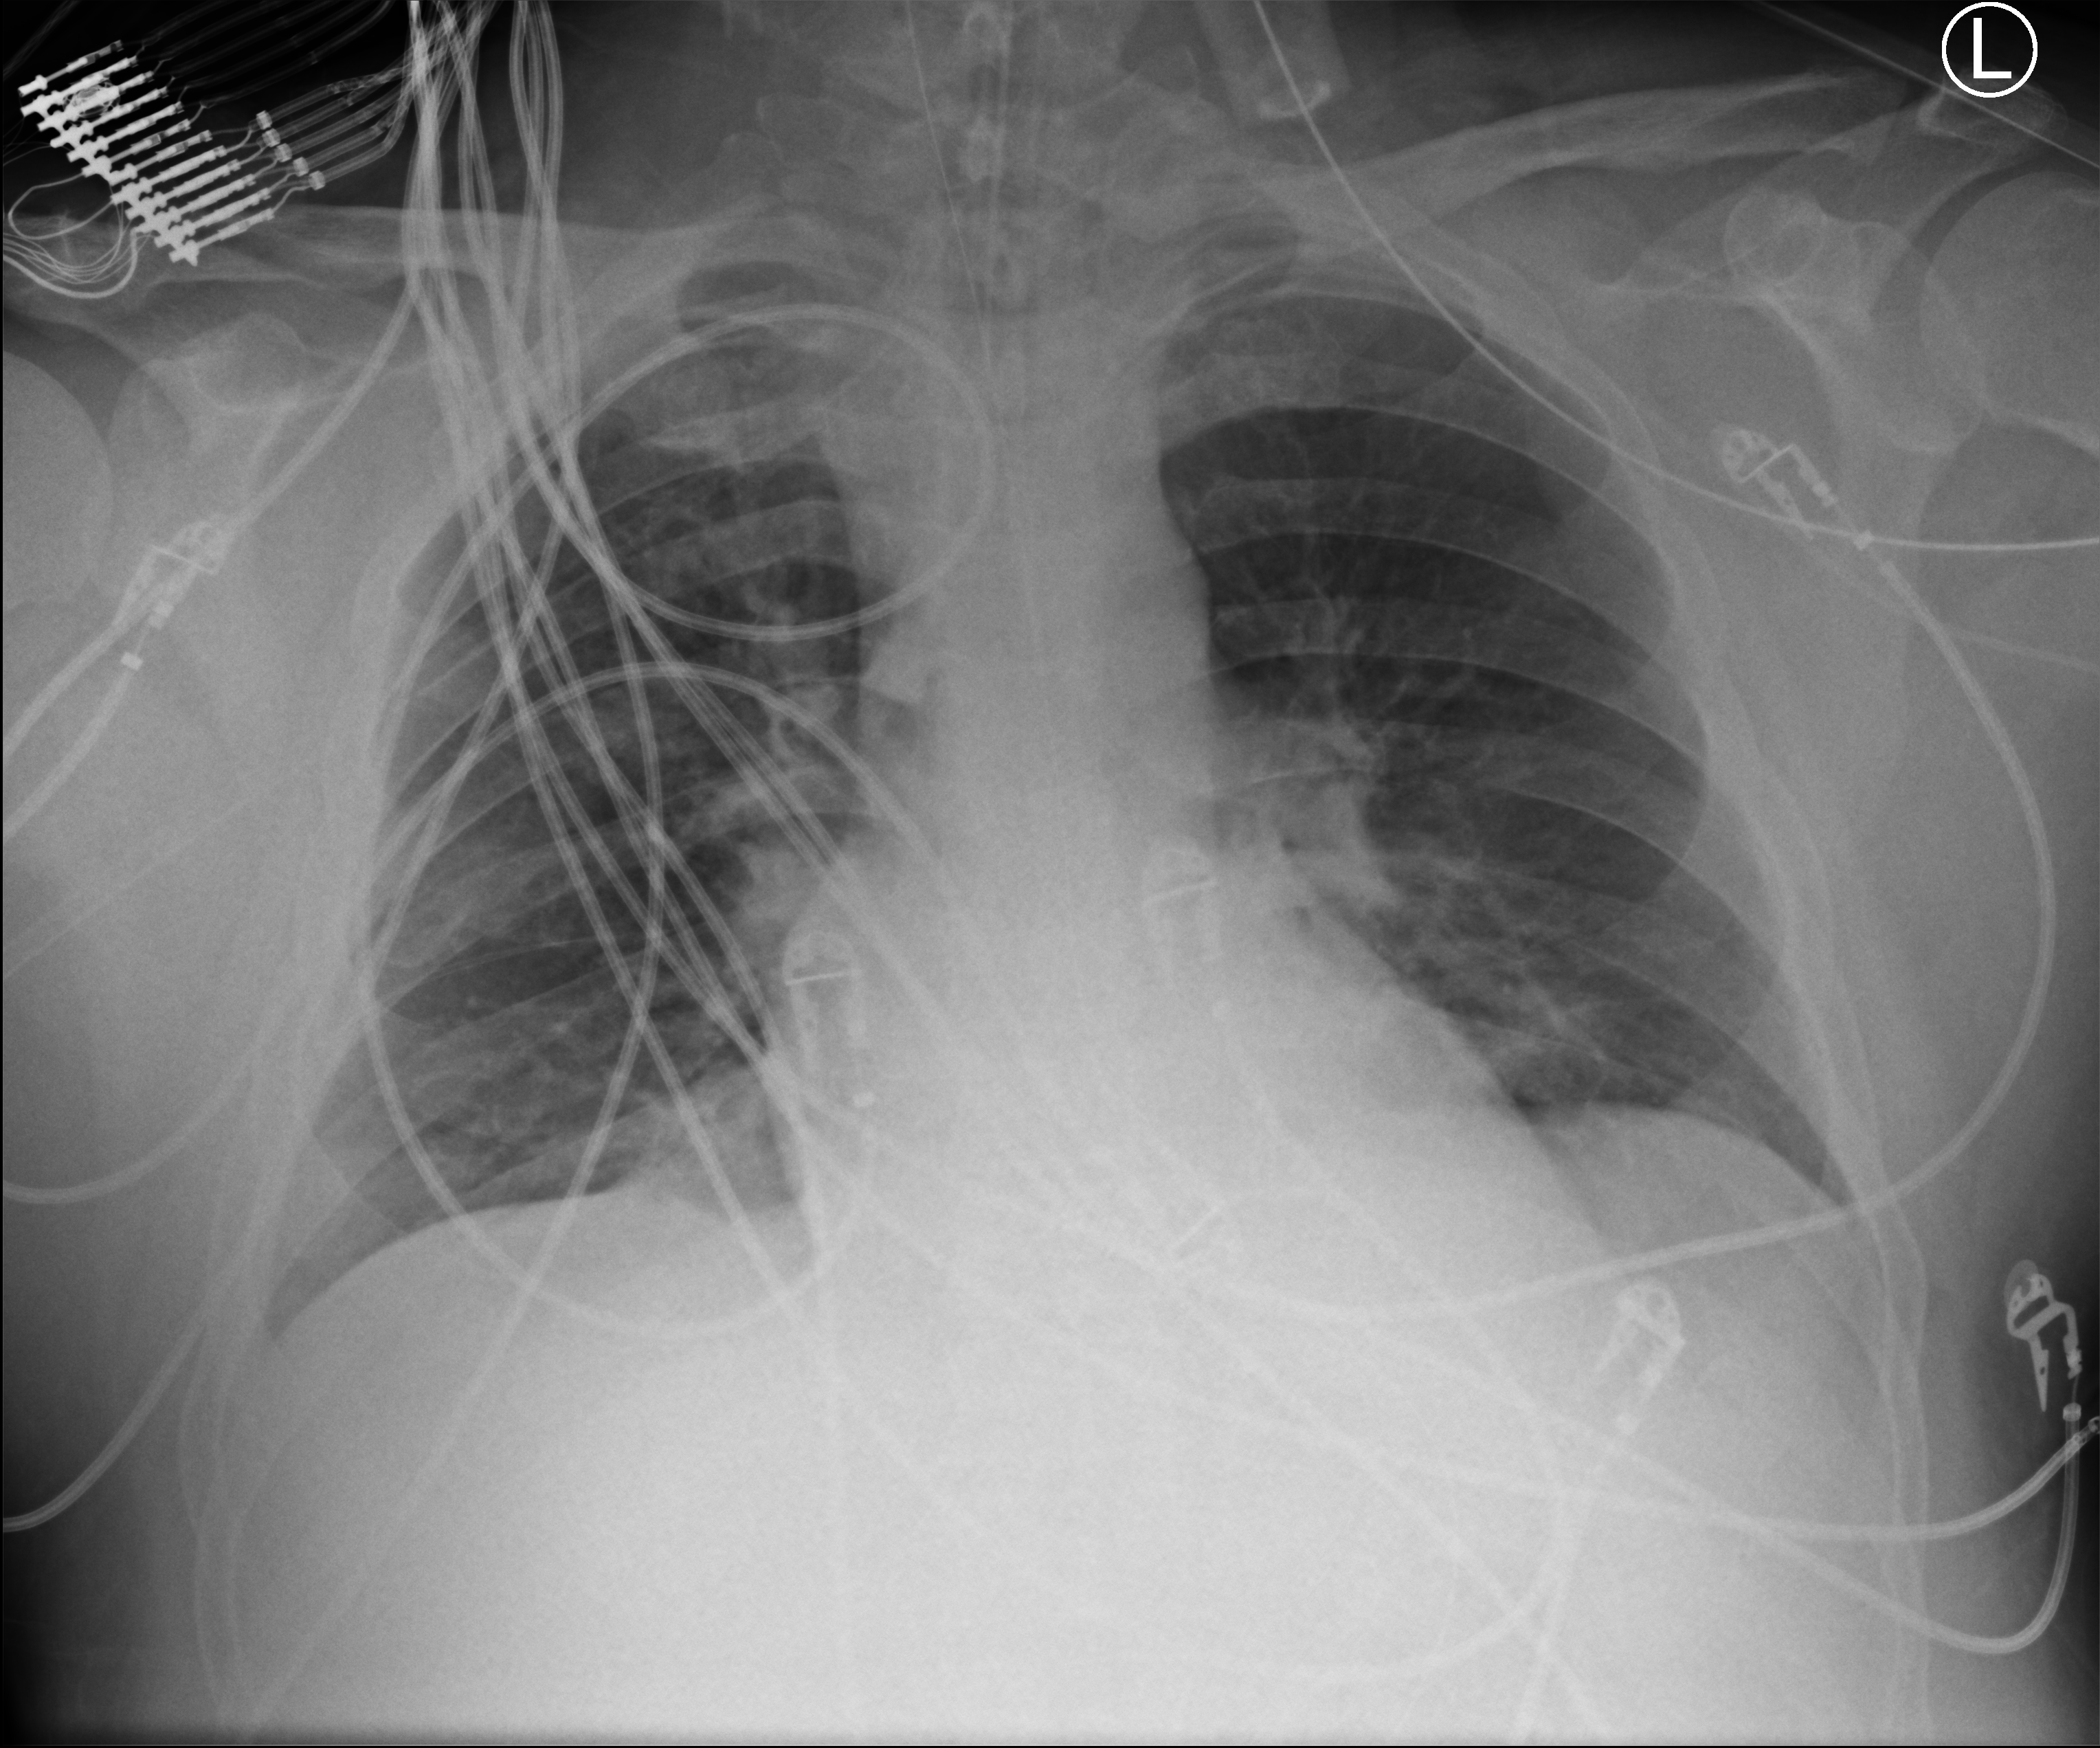
Portable chest radiograph, anteroposterior (AP) projection. Patient hospitalised with COVID-19; male, aged 18–59 years.
Hospital-stay facts (about this admission, not read from this image; timing relative to this image not recorded):
- mechanically ventilated during this hospital stay: yes